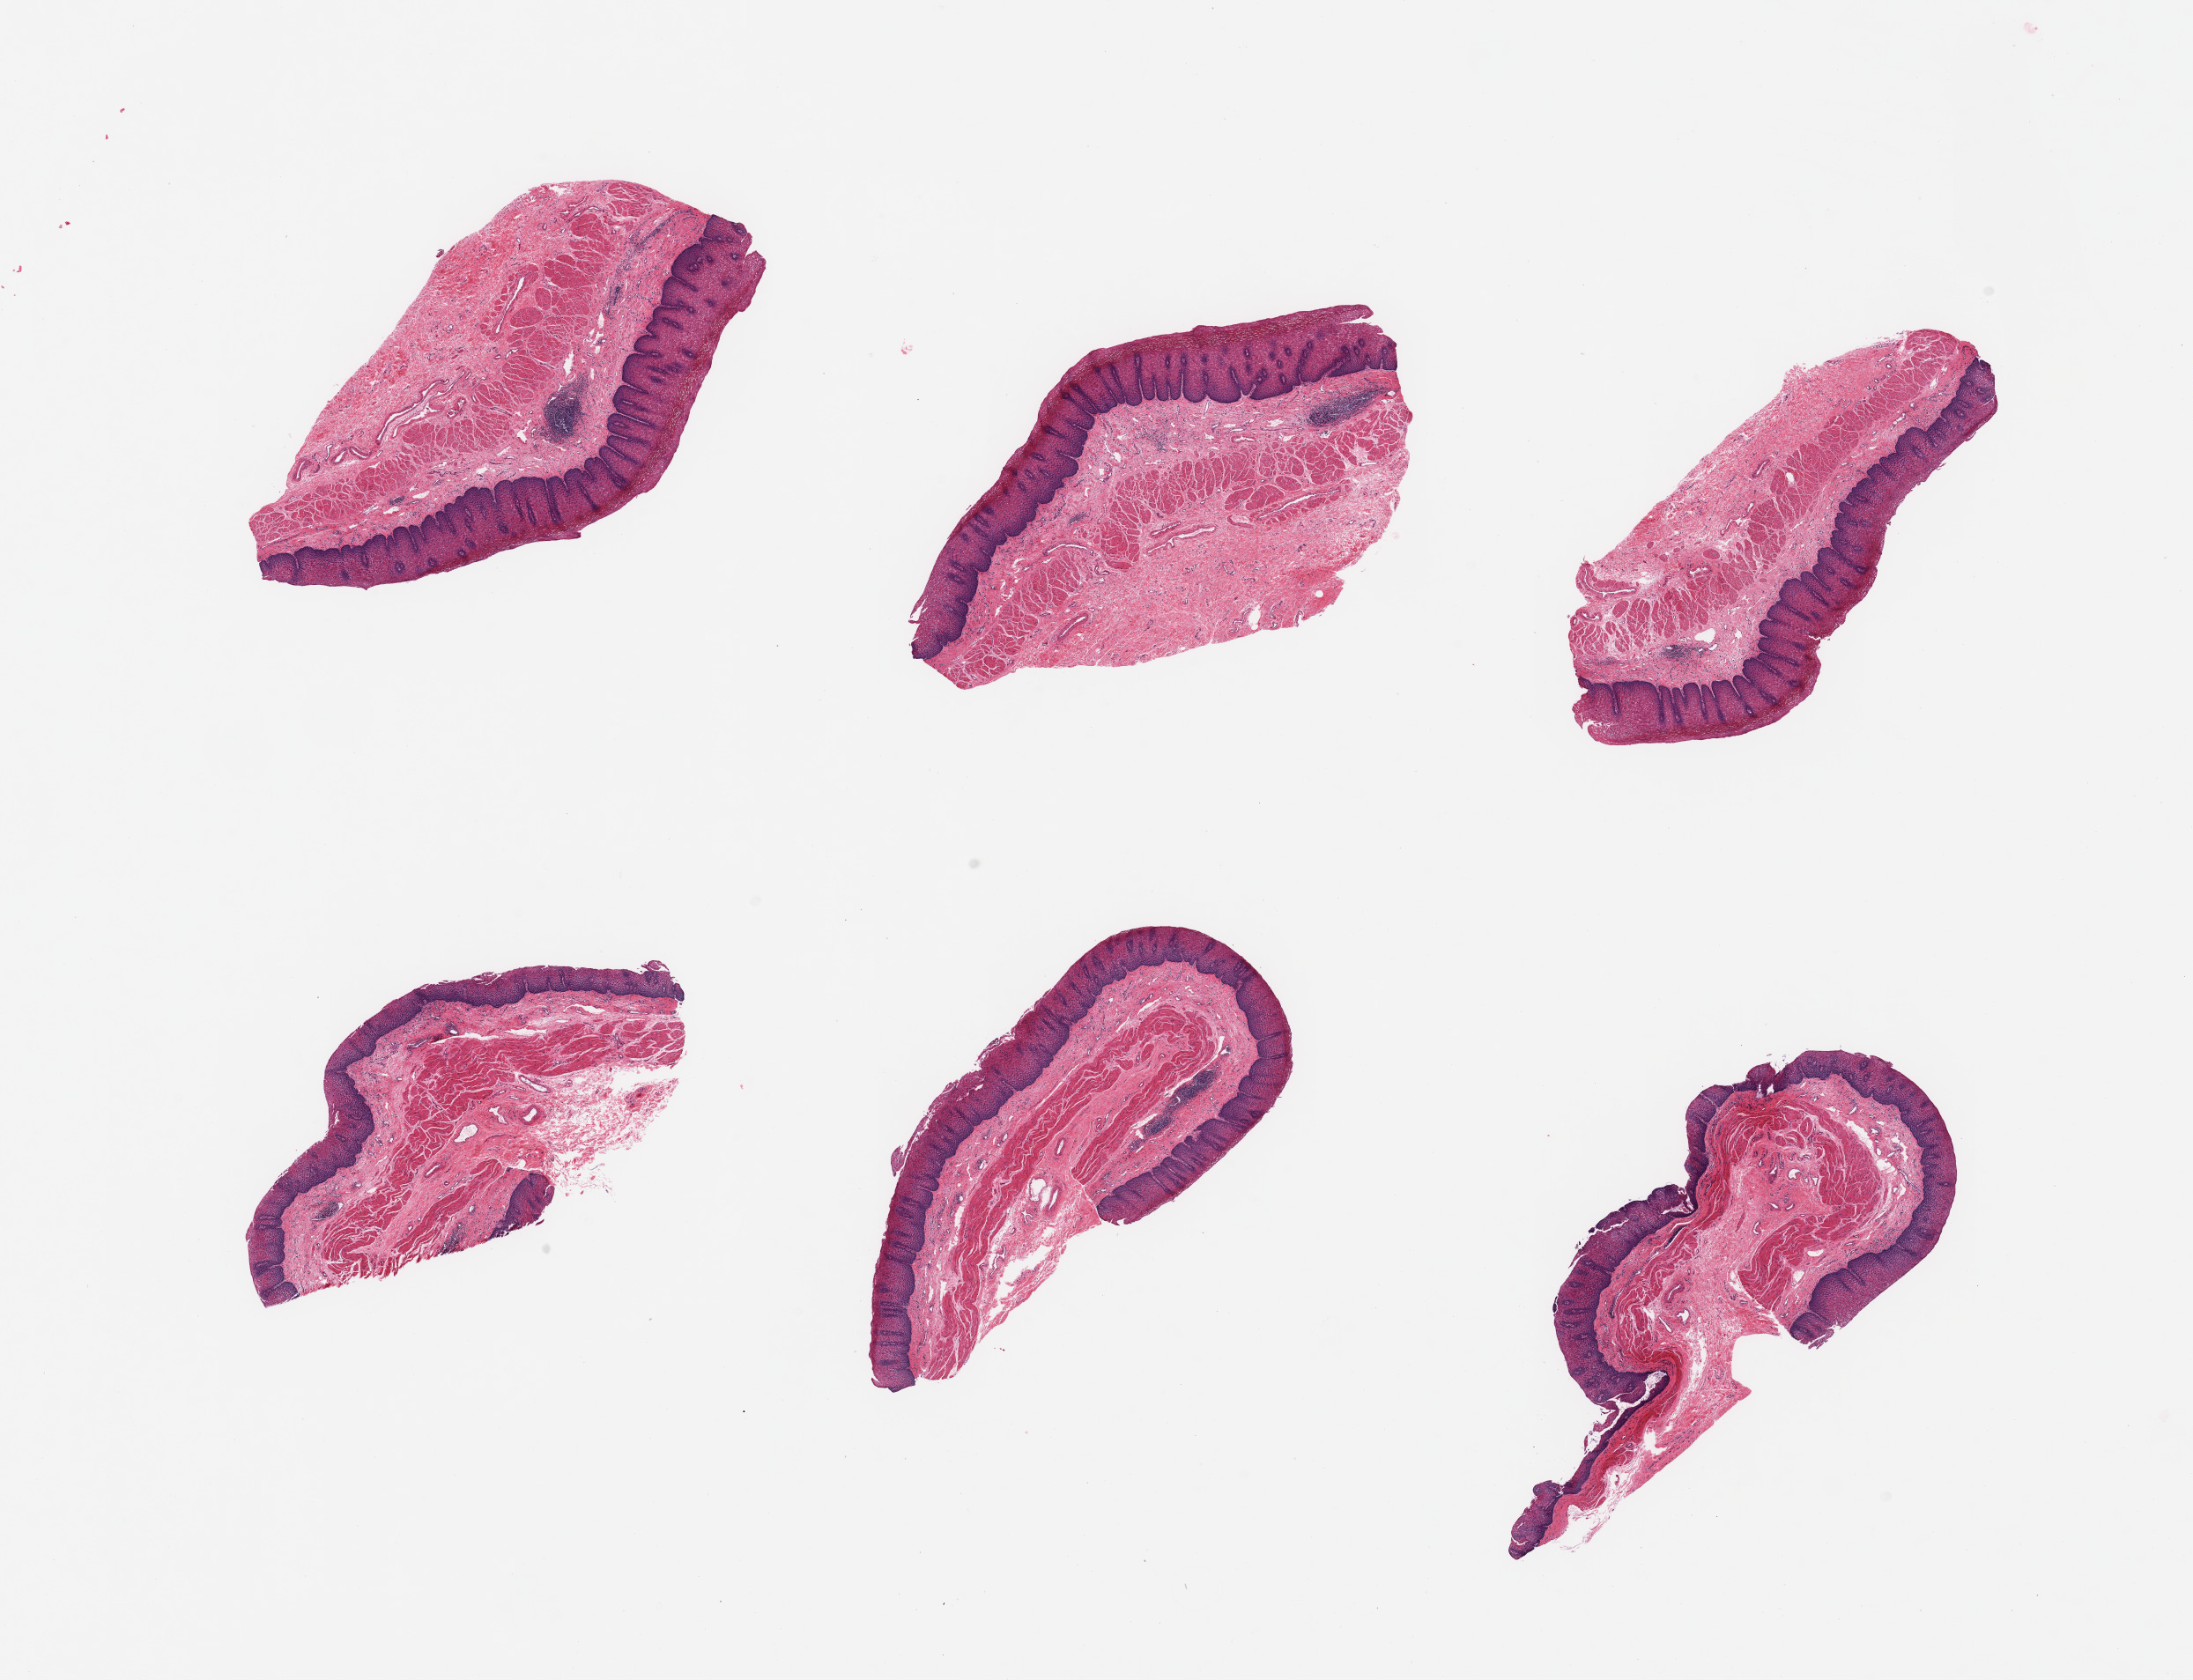
H&E whole-slide image, brightfield, a low-resolution overview of the entire scanned area, about 19.7 x 15.1 mm (acquisition: 20x scan); PAXgene-fixed paraffin-embedded (PFPE) section; target tissue: esophageal mucous membrane; tissue donor sample. Donor: male.
Pathologist's review note for this sample: 6 pieces; well dissected; mild to moderate squamous hyperplasia with focal lymphoid aggregates consistent with gastric reflux; no submucosal glands.